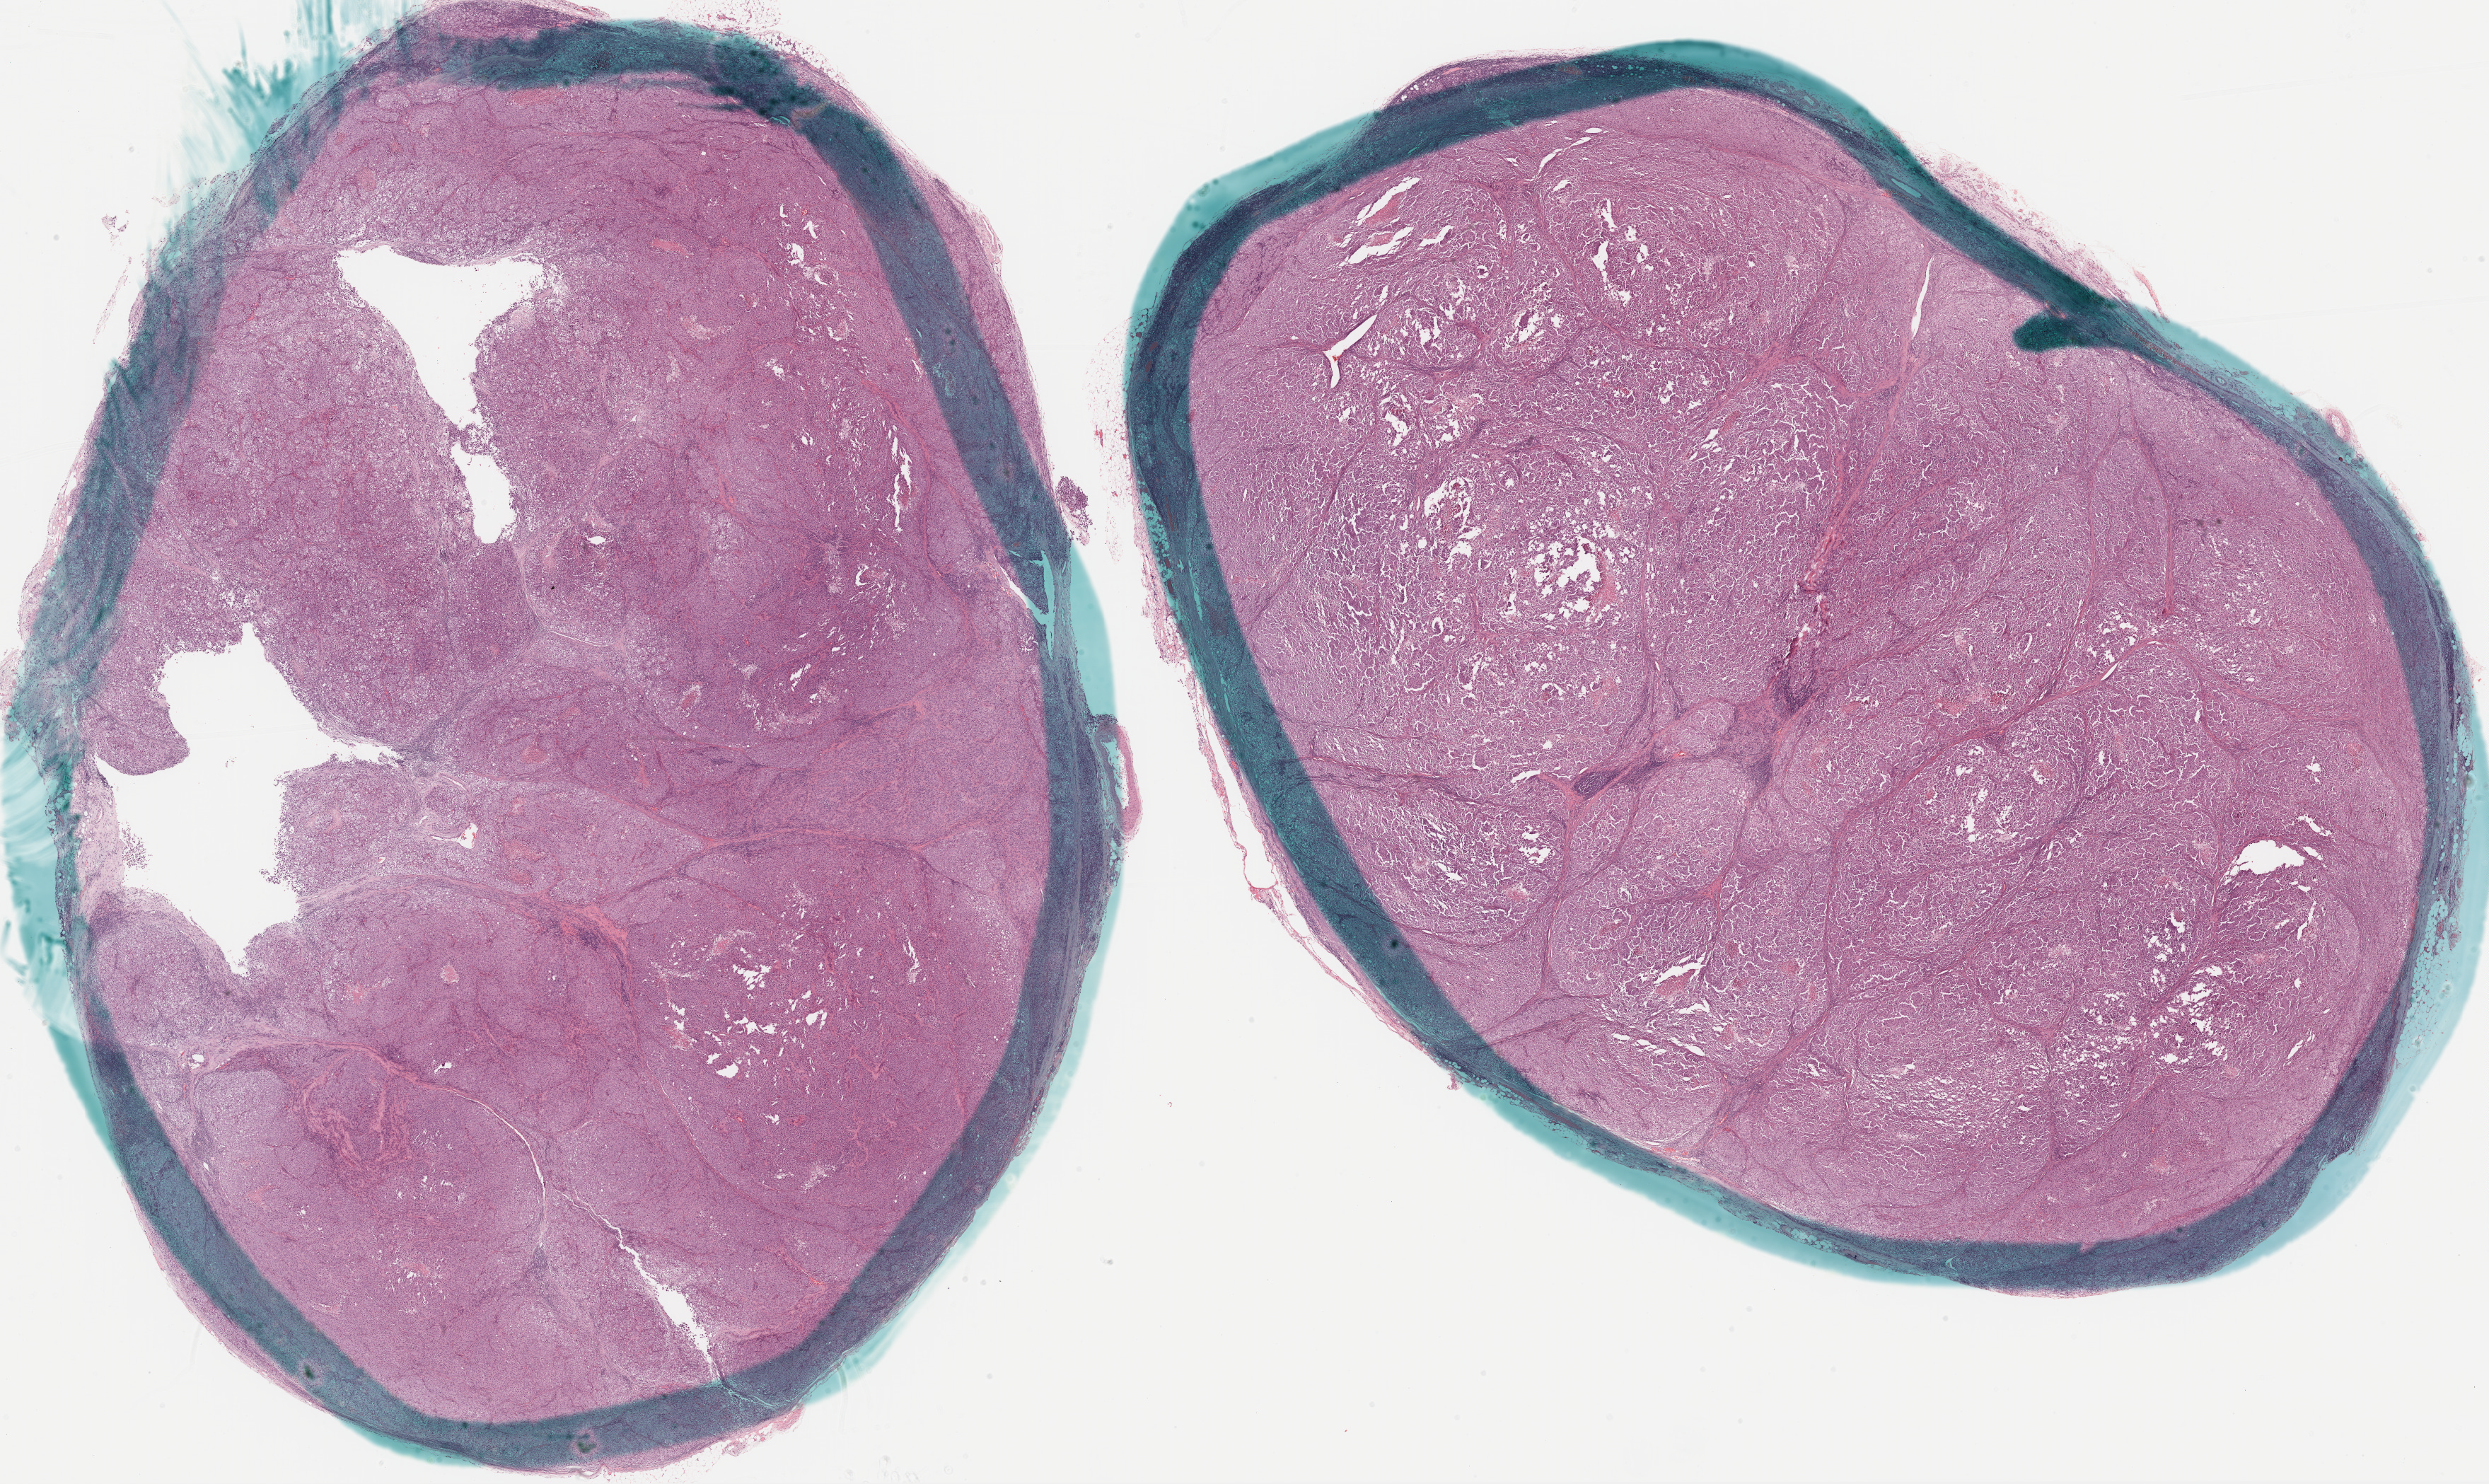
H&E whole-slide image, whole scanned area (about 28.4 x 16.9 mm, acquisition: 20x scan) shown as a low-resolution overview; formalin-fixed paraffin-embedded (FFPE) diagnostic section; metastatic tumour sample, sampled site not recorded. Patient: male, age at initial diagnosis 37 years.
• this section: metastatic tumour tissue
• patient diagnosis: Malignant melanoma, NOS